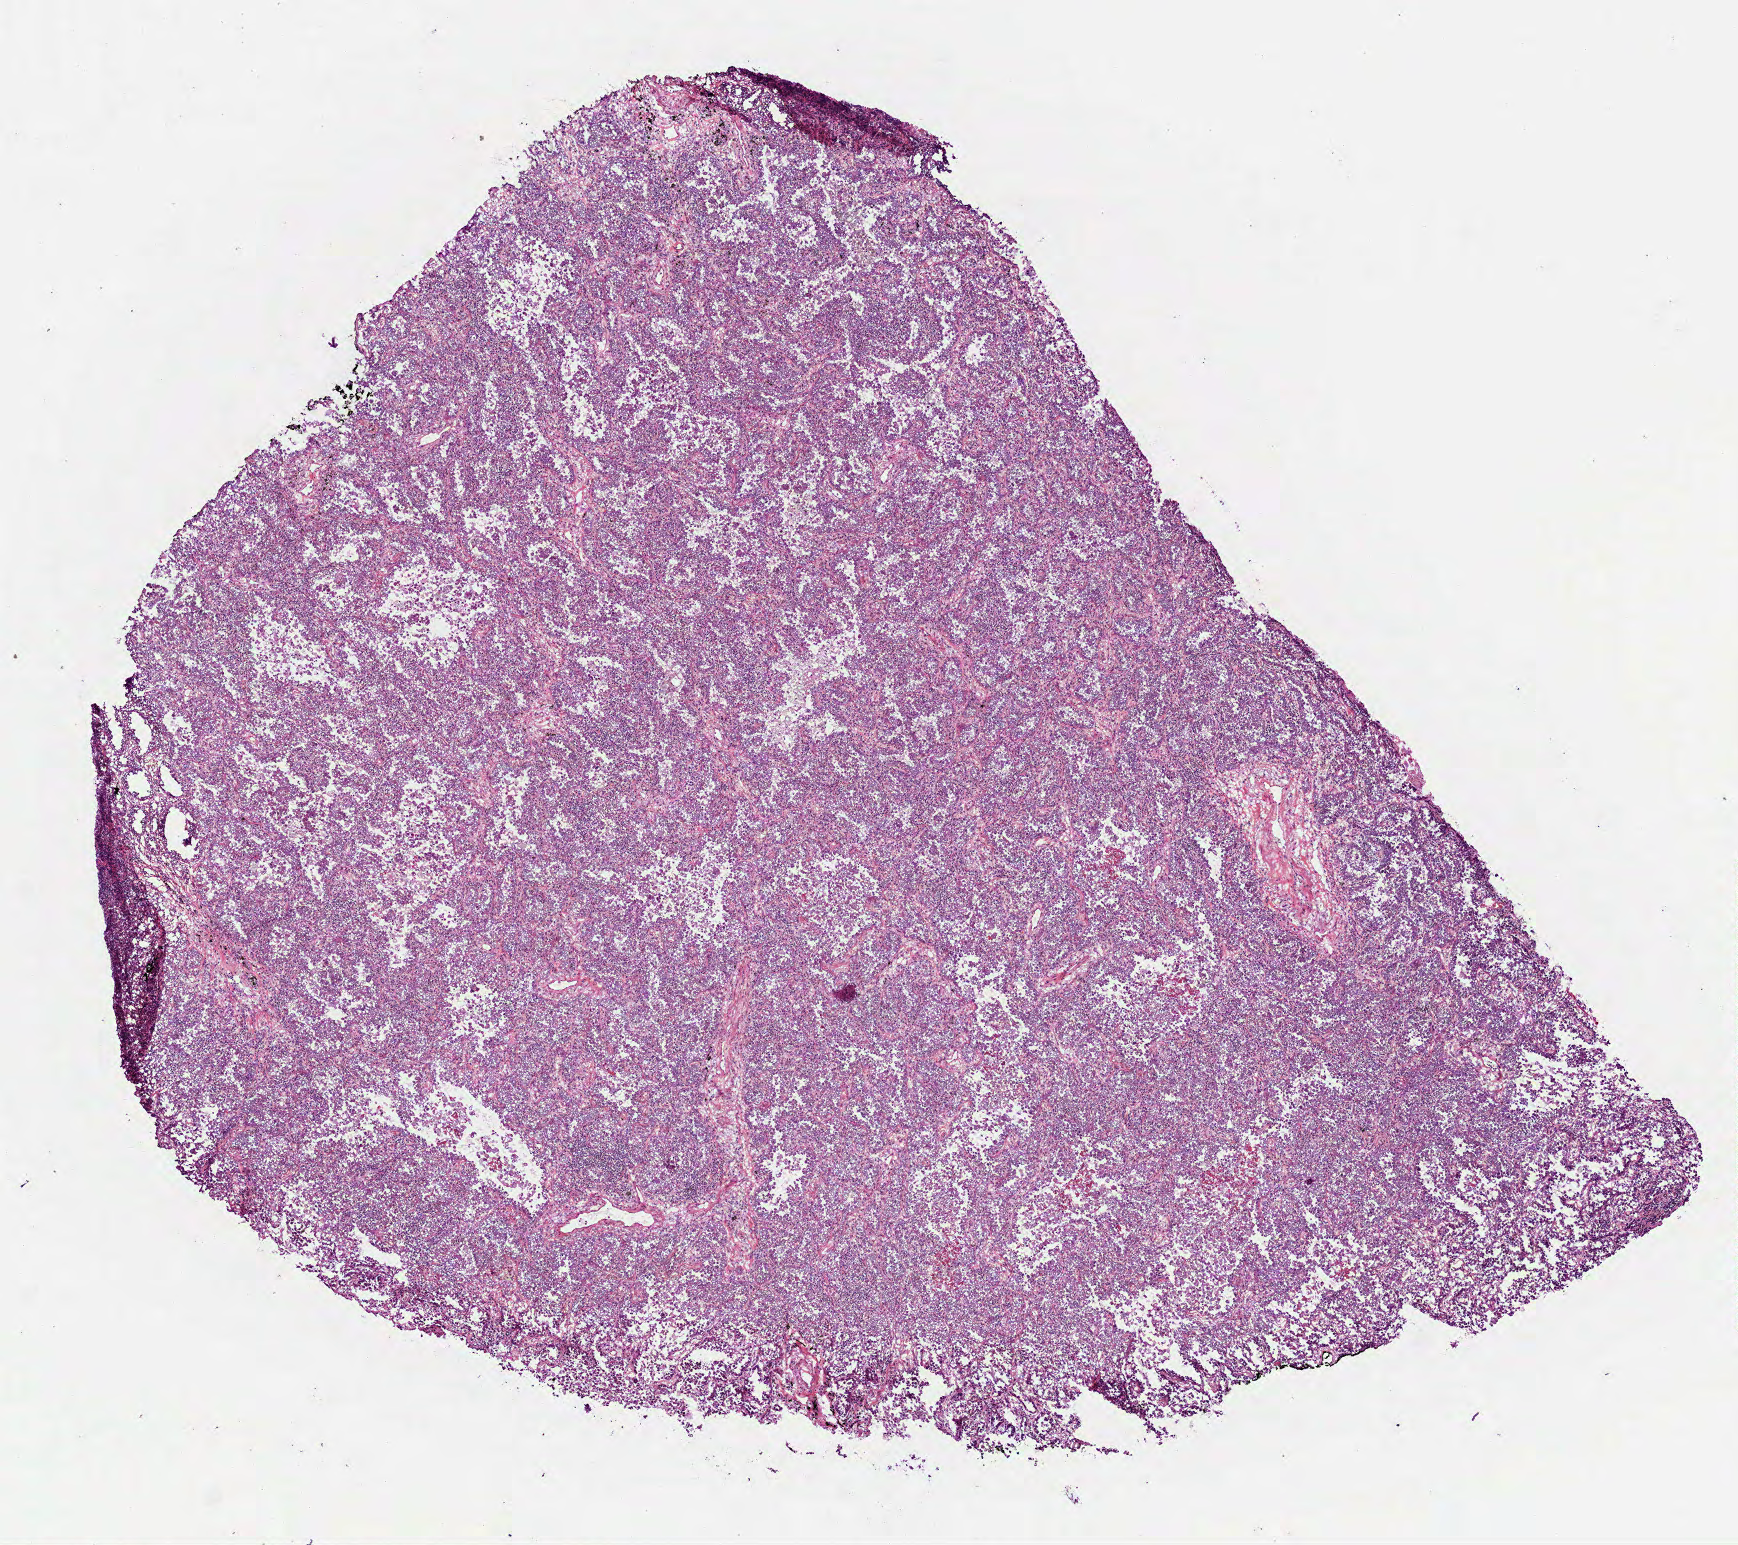
H&E-stained whole-slide image, low-resolution overview of the scanned area, about 7.0 x 6.2 mm (acquisition: 40x scan); frozen section from the bottom of the tissue portion; lung, primary tumour sample. Female patient; age at initial diagnosis 75 years. Pathologist review of this section (percent, as recorded): tumour cells 100%, tumour nuclei 80%, normal cells 0%, stromal cells 0%, necrosis 0%. Inflammatory infiltration, as recorded: lymphocyte infiltration 5%, monocyte infiltration 0%, neutrophil infiltration 0%.
Diagnosis: Adenocarcinoma with mixed subtypes (upper lobe, lung). AJCC pathologic stage: IIA (7th edition).